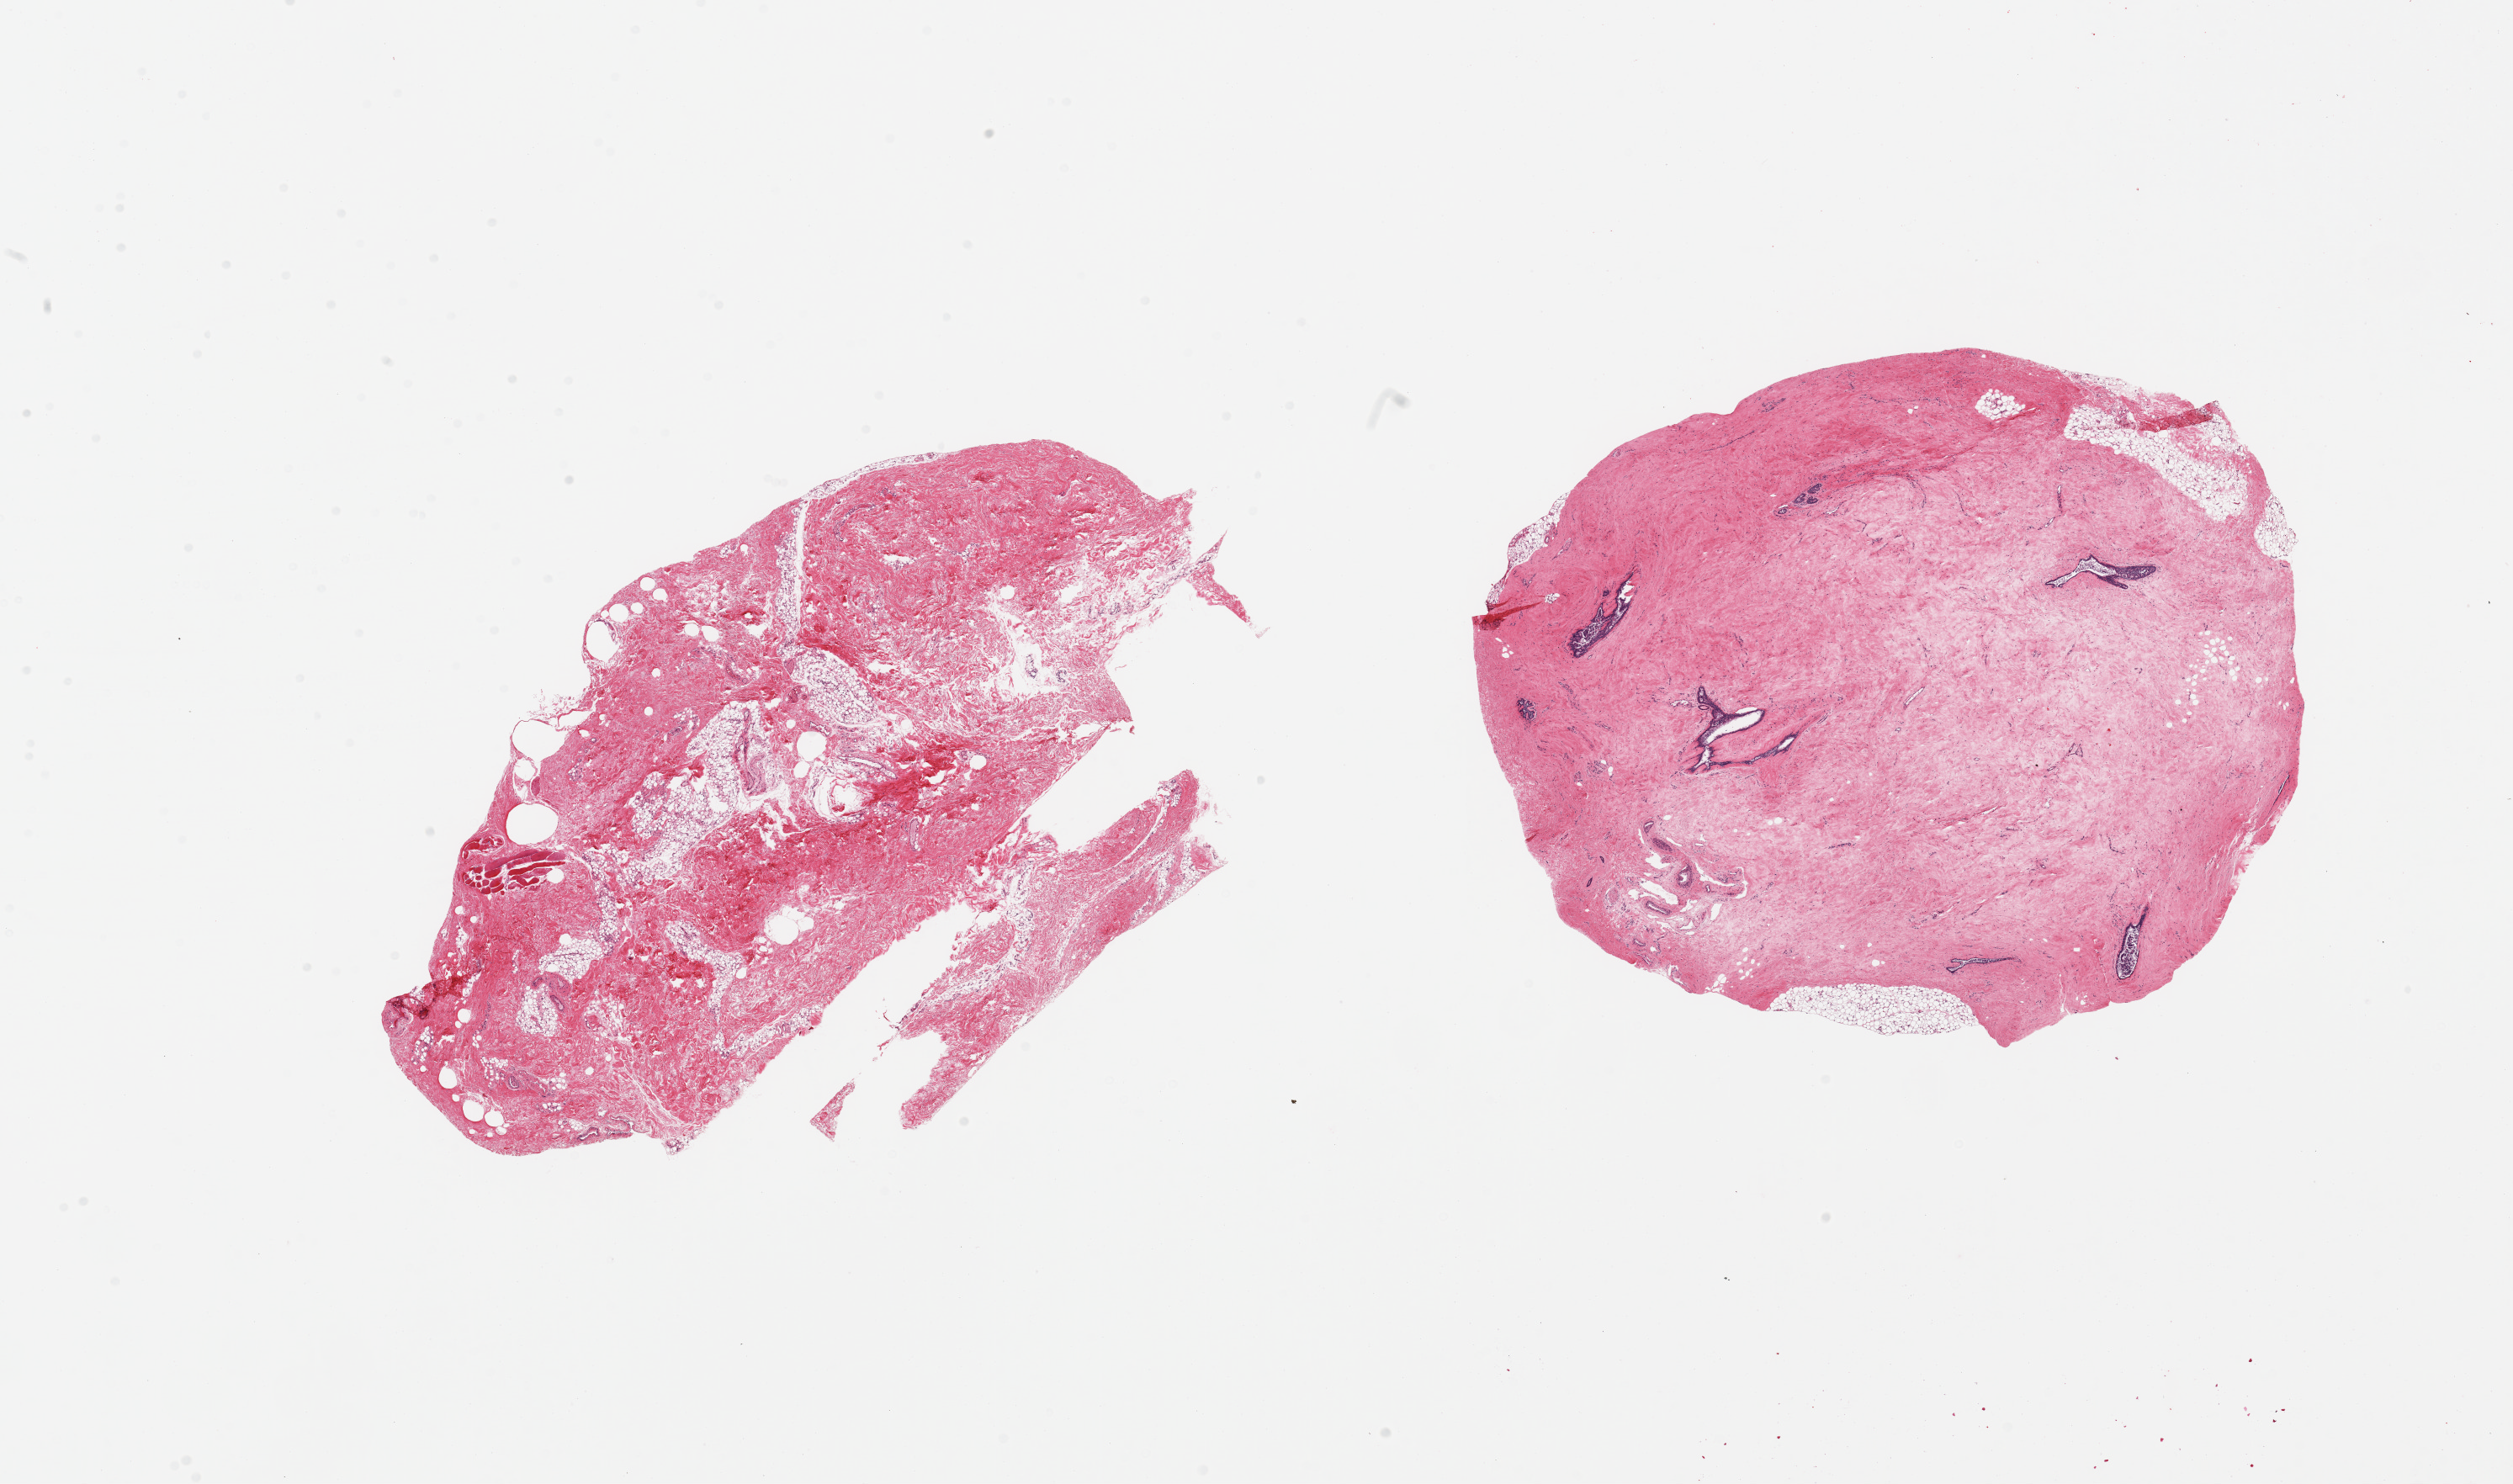
Whole-slide image, H&E stain — a low-resolution overview of the entire scanned area, about 23.6 x 14.0 mm (acquisition: 20x scan), PAXgene-fixed paraffin-embedded (PFPE) section, sampled site (target tissue): breast, tissue donor sample. Donor: male.
Pathologist's review note for this sample: 2 pieces; 1 piece has gynecomastoid changes (ducts & fibrous tissue); other piece has fibrous, skeletal muscle and fat, no mammary tissue.